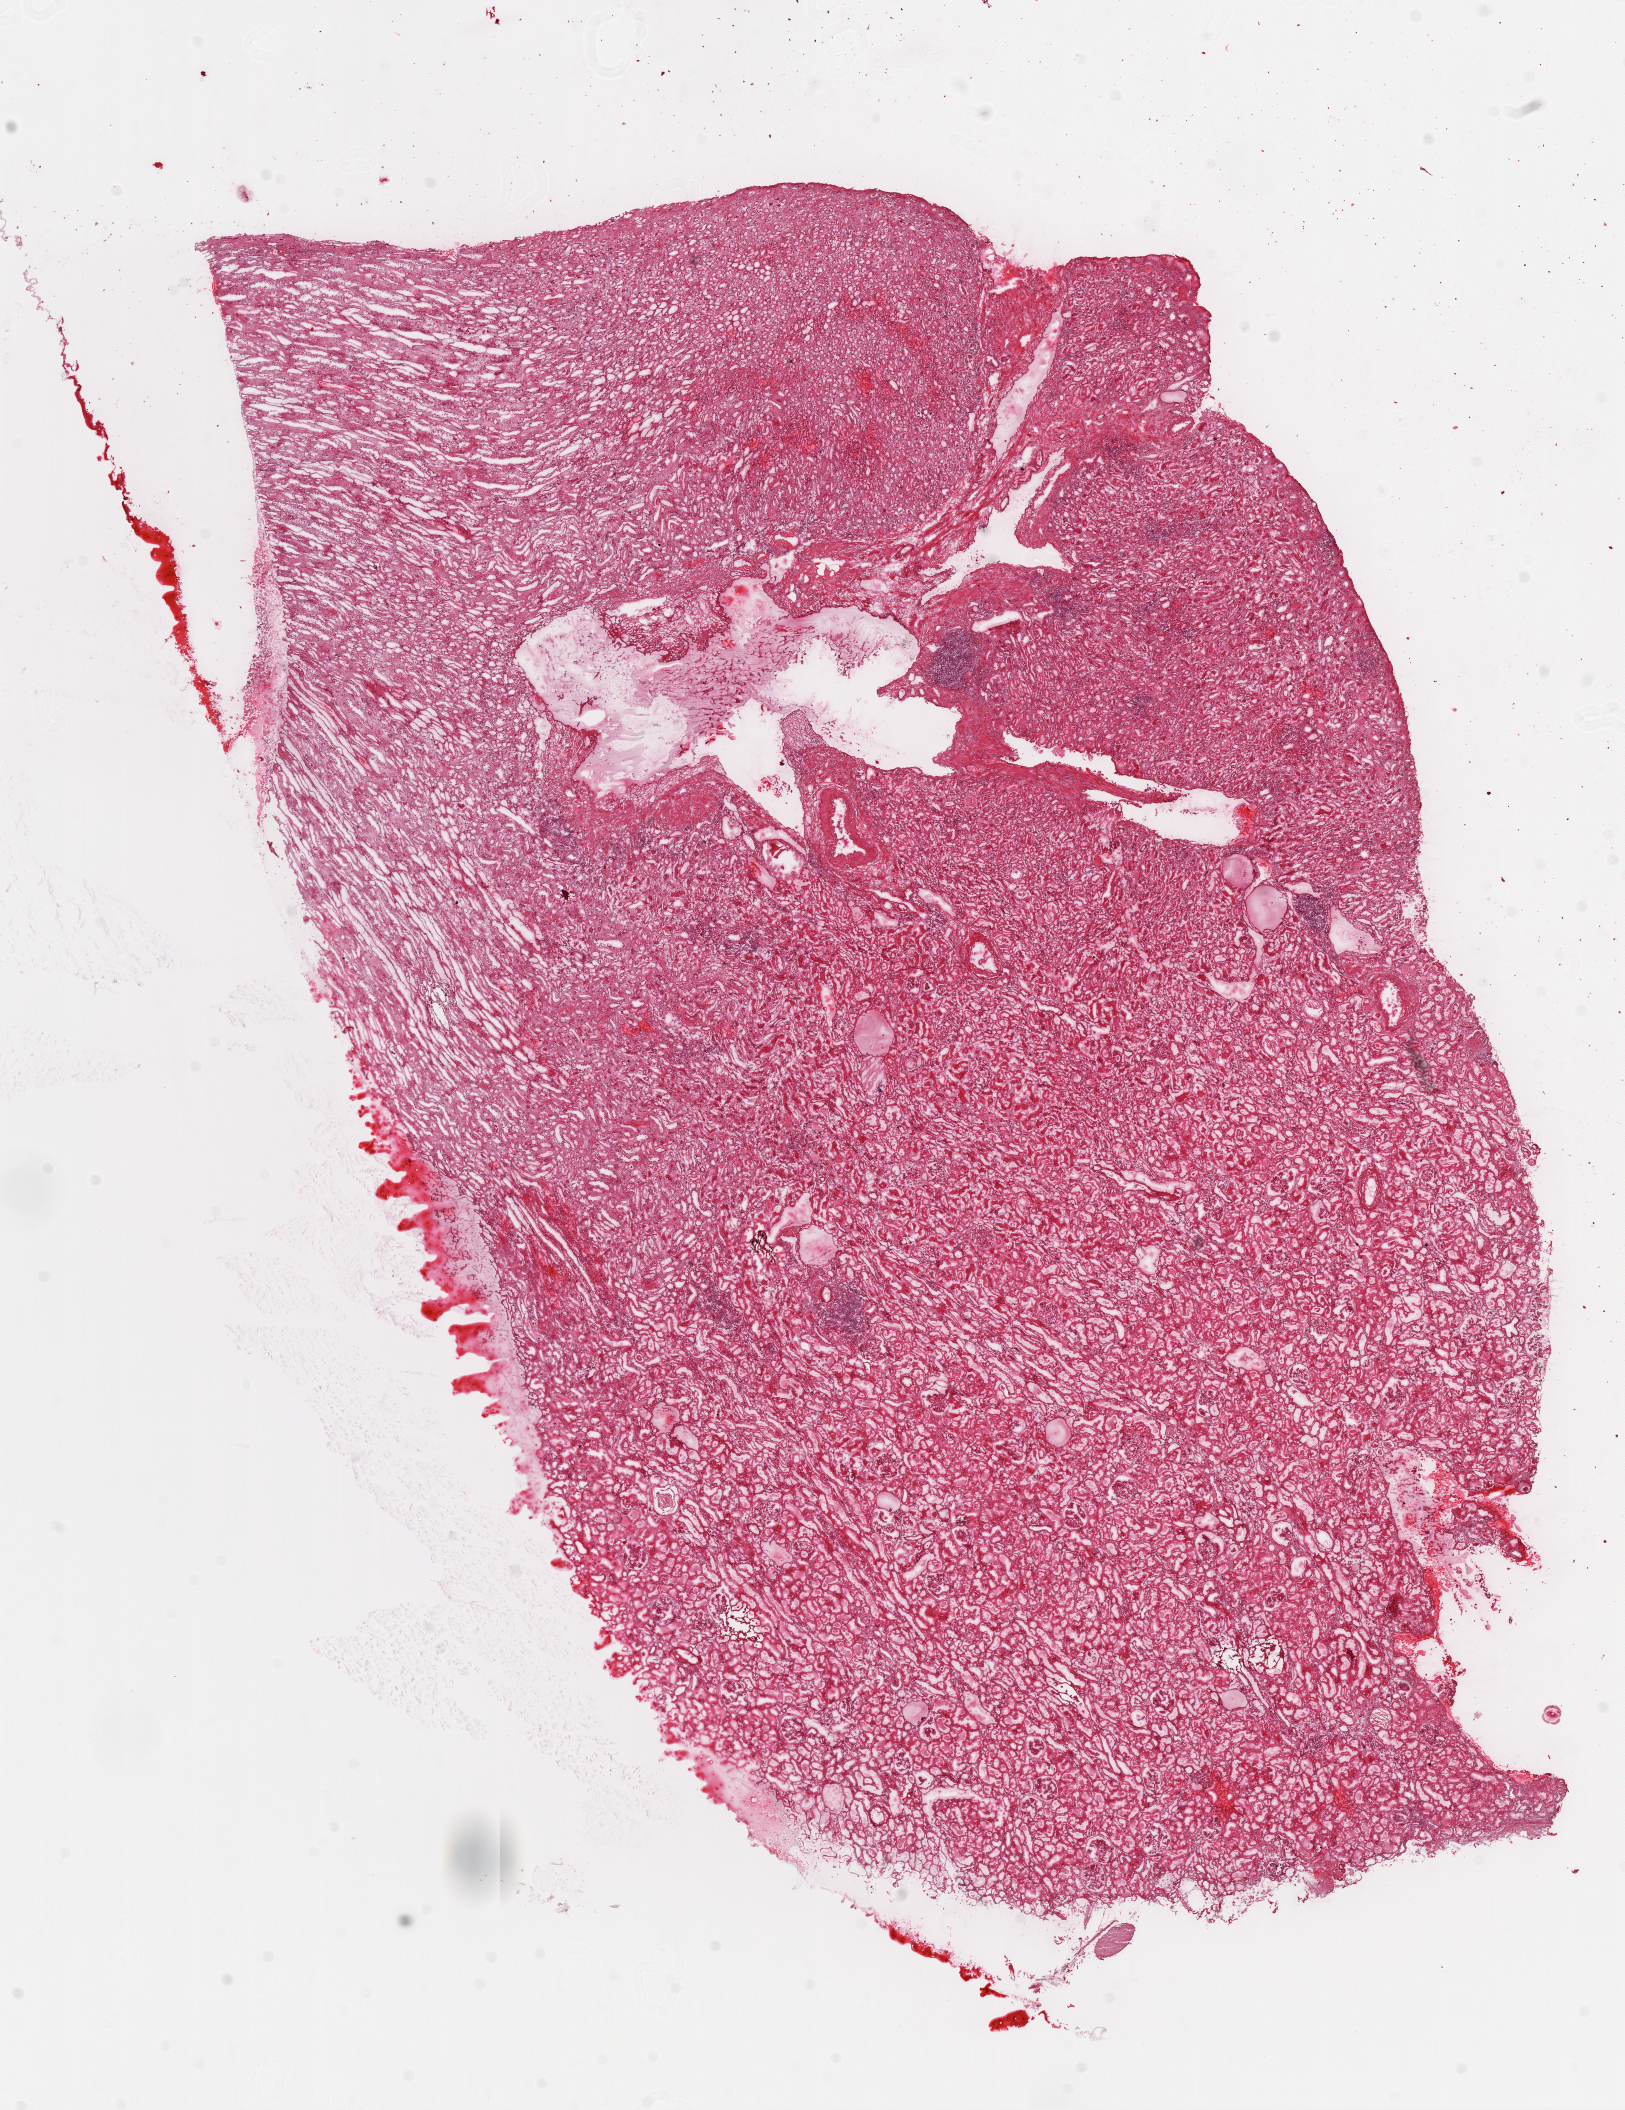
Digitized Hematoxylin and eosin (H&E) stained tissue section (whole slide), shown as a low-resolution overview of the whole scanned area (about 13.0 x 16.9 mm, acquisition: 20x scan); frozen section from the top of the tissue portion; sample: solid tissue normal (non-tumour tissue), kidney. Patient: female, age at initial diagnosis 76 years.
This section: solid tissue normal (non-tumour) sample from the same patient. Patient diagnosis: Clear cell adenocarcinoma, NOS.